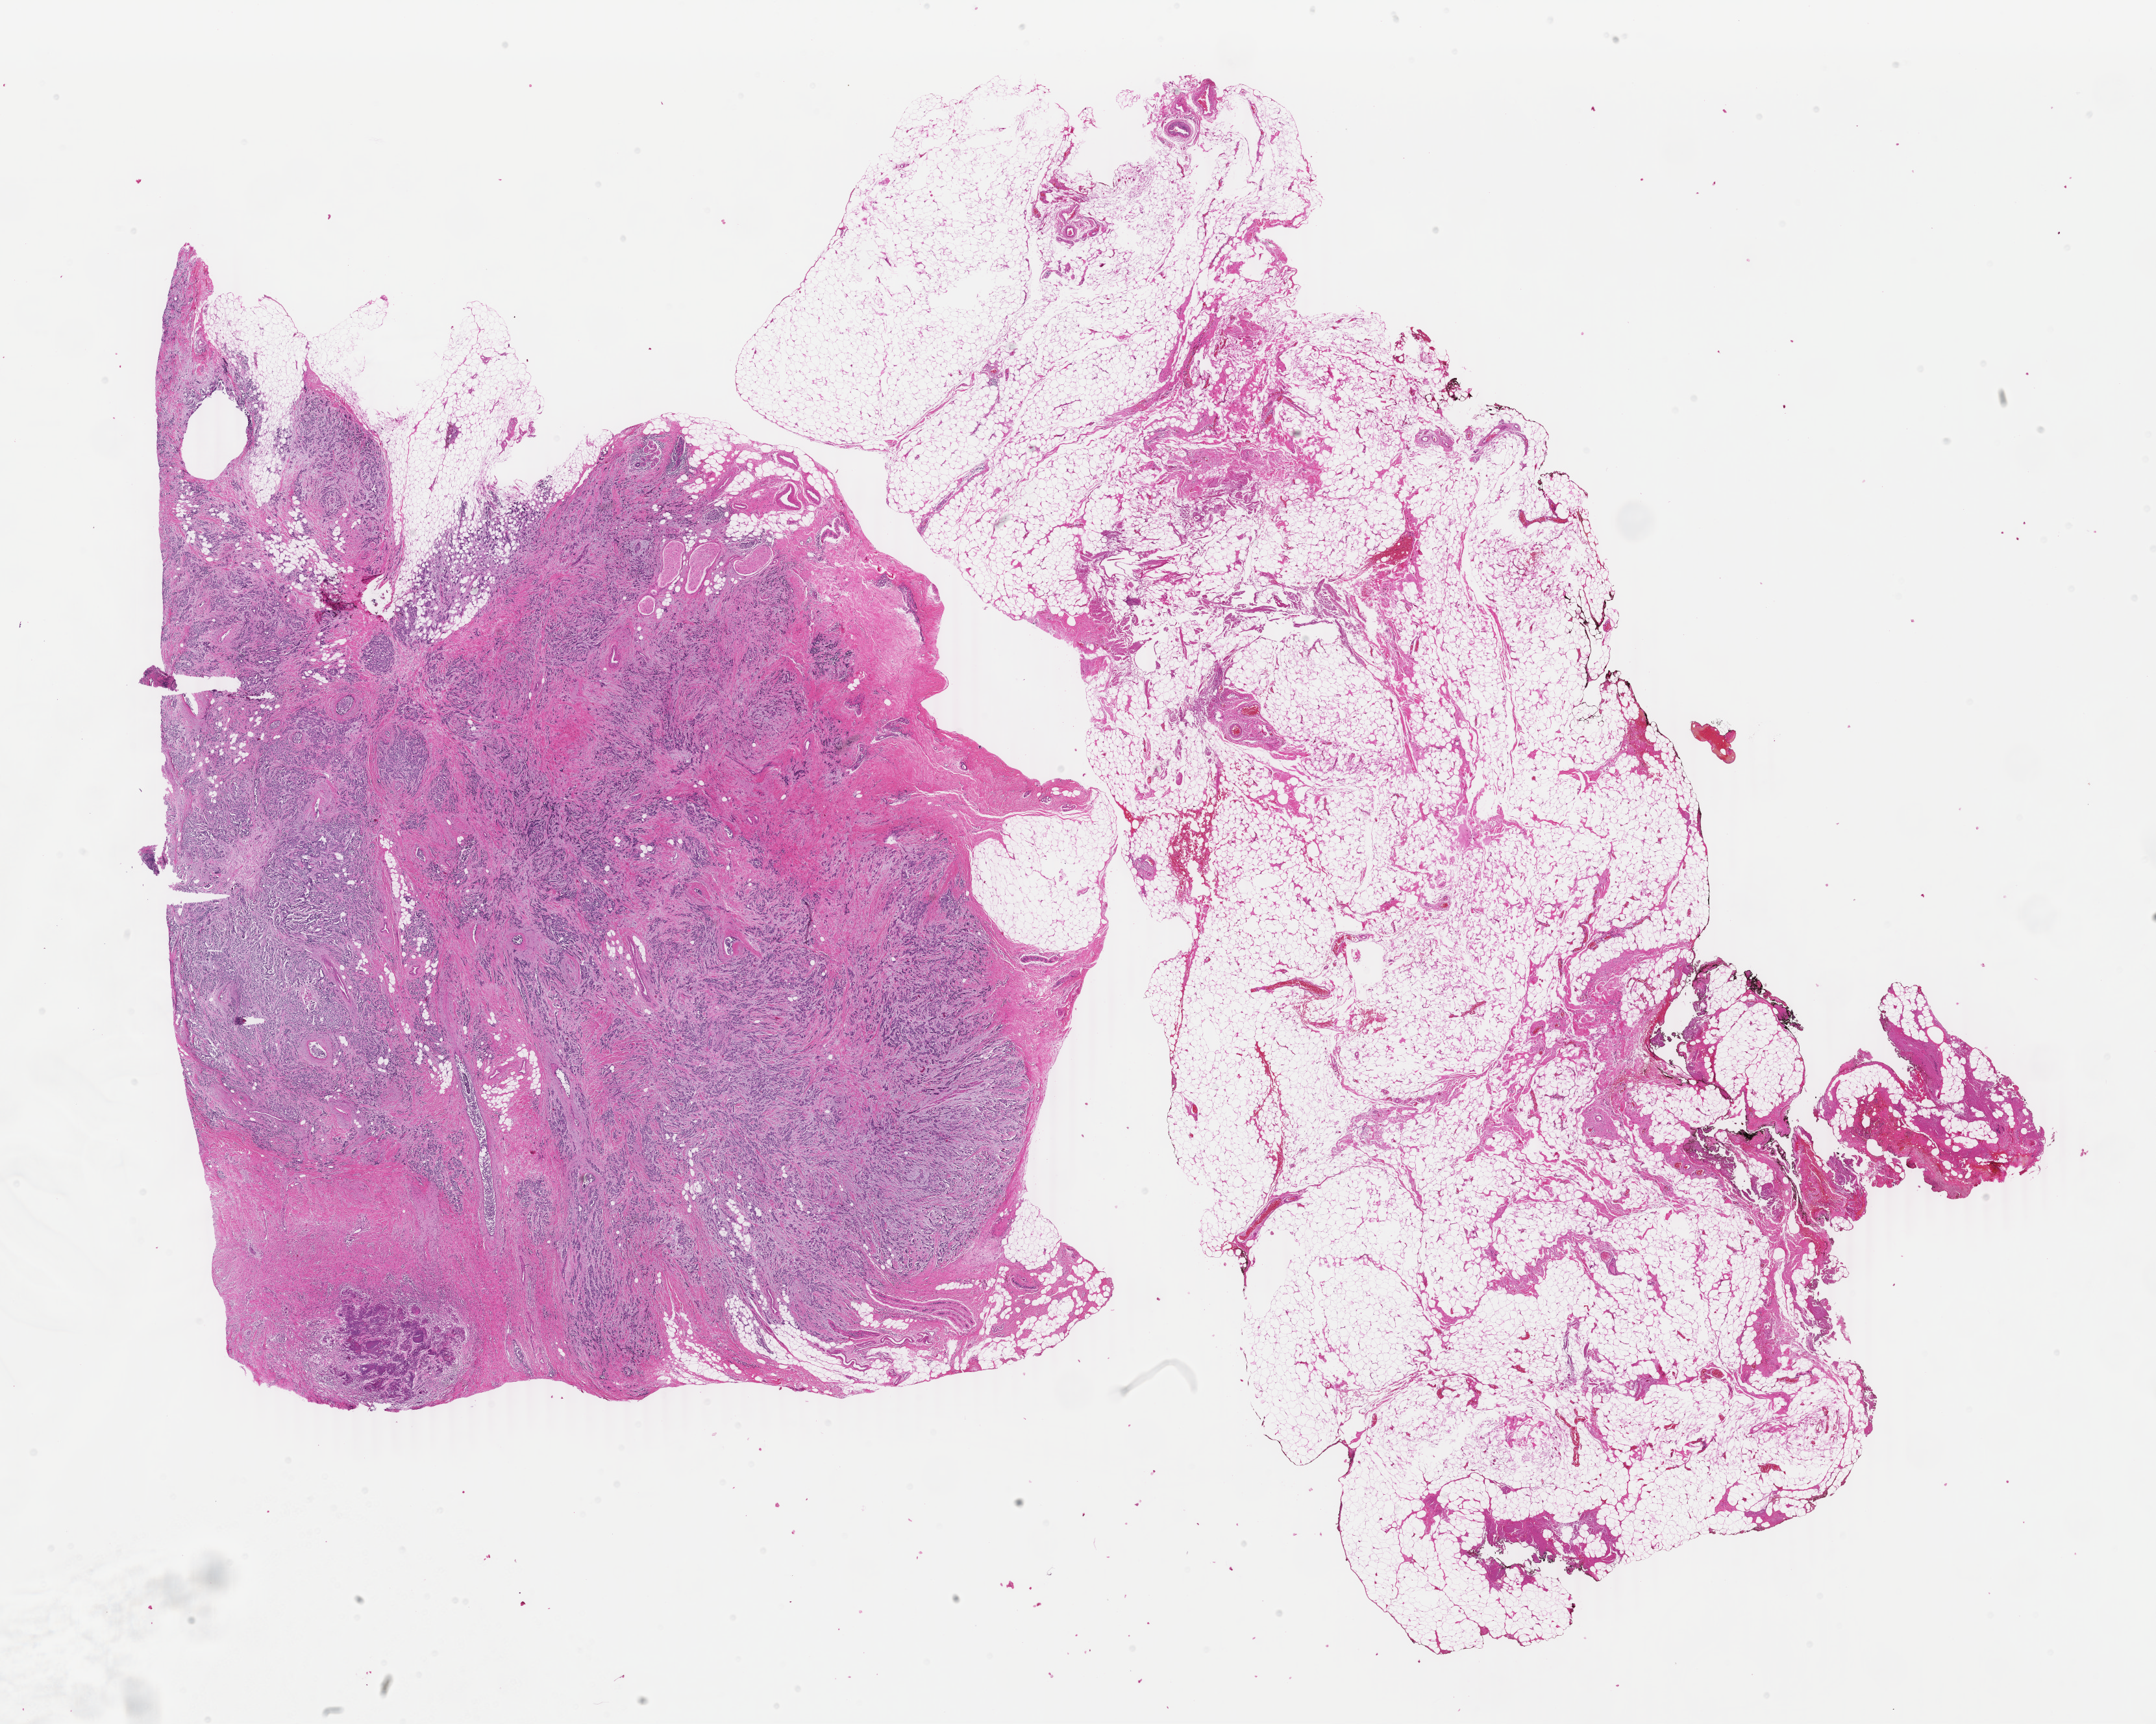
Digitized Hematoxylin and eosin (H&E) stained tissue section (whole slide) — shown as a low-resolution overview of the whole scanned area (about 26.4 x 21.1 mm); formalin-fixed paraffin-embedded (FFPE) diagnostic section; primary tumour sample from the breast. Female patient; age at initial diagnosis 71 years.
Diagnosis: Infiltrating duct carcinoma, NOS. AJCC pathologic stage: IIA (6th edition). Lymph nodes positive (case pathology): 0 of 2 examined.